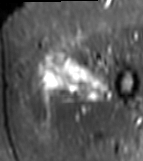
MRI of an extremity soft-tissue mass, one axial slice. Position 17 of 81 along the scan axis. STIR. MR volume resampled by the dataset authors to the PET/CT grid (not the native acquisition matrix). 143 × 161 image matrix, field of view 140 × 157 mm. Female patient. Case-level facts recorded for this patient, not image findings: histological type: myxofibrosarcoma; grade: intermediate; site of the primary tumour: left thigh.
Outlined on this slice (expert contour drawn on MRI and transferred to this co-registered scan by the dataset authors):
- gross tumour volume including surrounding oedema: box from (x=33, y=53) to (x=109, y=105) px
- gross tumour volume (mass): (x=40, y=53)–(x=102, y=104)